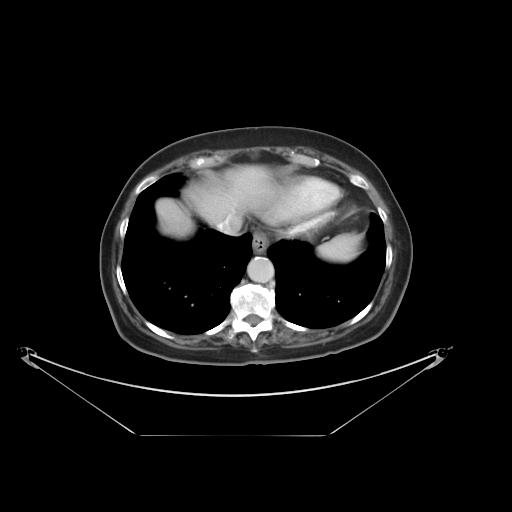
Contrast-enhanced abdominal CT, one axial slice; slice 32 of 36 in the series (ordered by position); reconstruction kernel STANDARD; 120 kVp; intravenous contrast given; soft-tissue window (W 400 / L 40 HU); 512 × 512 image matrix, field of view 500 × 500 mm. Female patient, age 70 years. From the clinical record (not read from this slice): diagnosis: colorectal cancer liver metastases, imaged before liver resection; multiple liver metastases: no; largest metastasis: 2.5 cm; chemotherapy before resection: no.
Outlined on this slice (manually delineated by an expert):
- hepatic veins: box from (x=217, y=210) to (x=234, y=233) px
- liver: (x=158, y=169)–(x=275, y=237)
- planned liver remnant (the part of the liver to remain after resection): (x=158, y=169)–(x=275, y=237)